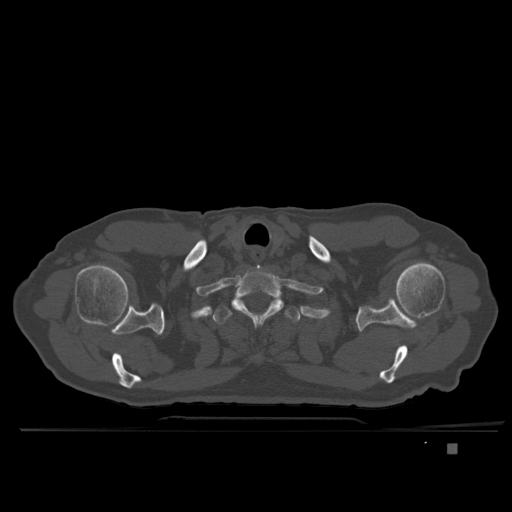
CT including the spine, one axial slice. Slice 321 of 435 in the series (ordered by position). Bone window (W 1800 / L 400 HU). 1.5 mm slice thickness. 512 × 512 image matrix. Patient: male, 73 years. Case-level facts recorded for this patient, not image findings: primary cancer: skin.
Structures marked on this image (semi-automatically segmented with operator editing):
- T1 vertebra: bounding box (x1, y1, x2, y2) in pixels: (231, 268, 284, 327)
- T2 vertebra: (214, 296, 300, 325)